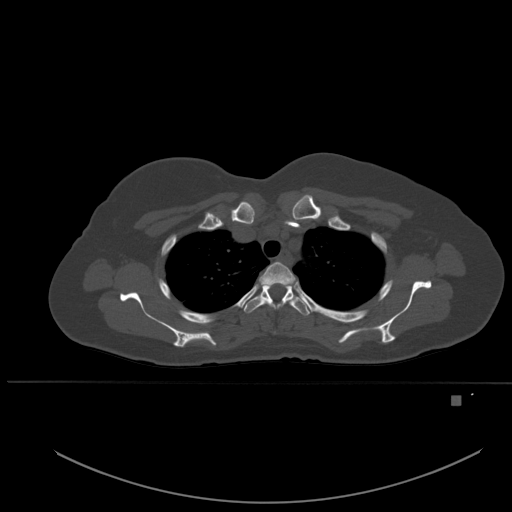
CT including the spine, one axial slice. Bone window (W 1800 / L 400 HU). 512 × 512 image matrix, field of view 443 × 443 mm. Female patient, age 49 years. Case-level facts recorded for this patient, not image findings: primary cancer: breast.
Structures marked on this image (semi-automatically segmented with operator editing):
- T2 vertebra: bounding box (x1, y1, x2, y2) in pixels: (259, 262, 296, 307)
- T3 vertebra: (244, 283, 310, 316)